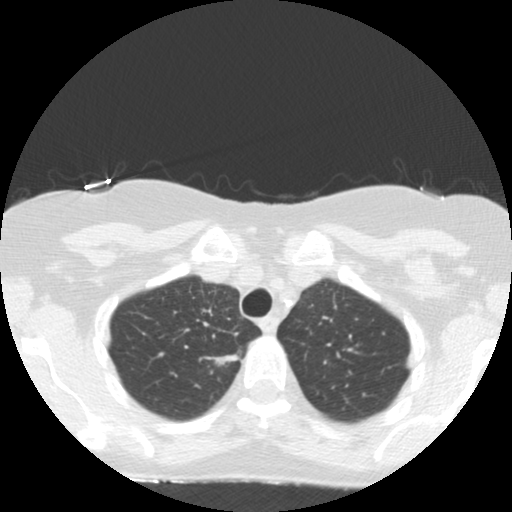
Low-dose screening chest CT, one axial slice; position 126 of 155 along the scan axis; reconstruction kernel STANDARD; lung window (W 1500 / L -600 HU); 2.5 mm slice thickness; 512 × 512 image matrix, field of view 300 × 300 mm.
Annotated regions visible in this slice (outlined manually by an expert reader):
- lesion 1 (tumor, upper lobe of right lung): bounding box <203,354,239,366> (left, top, right, bottom; pixels)